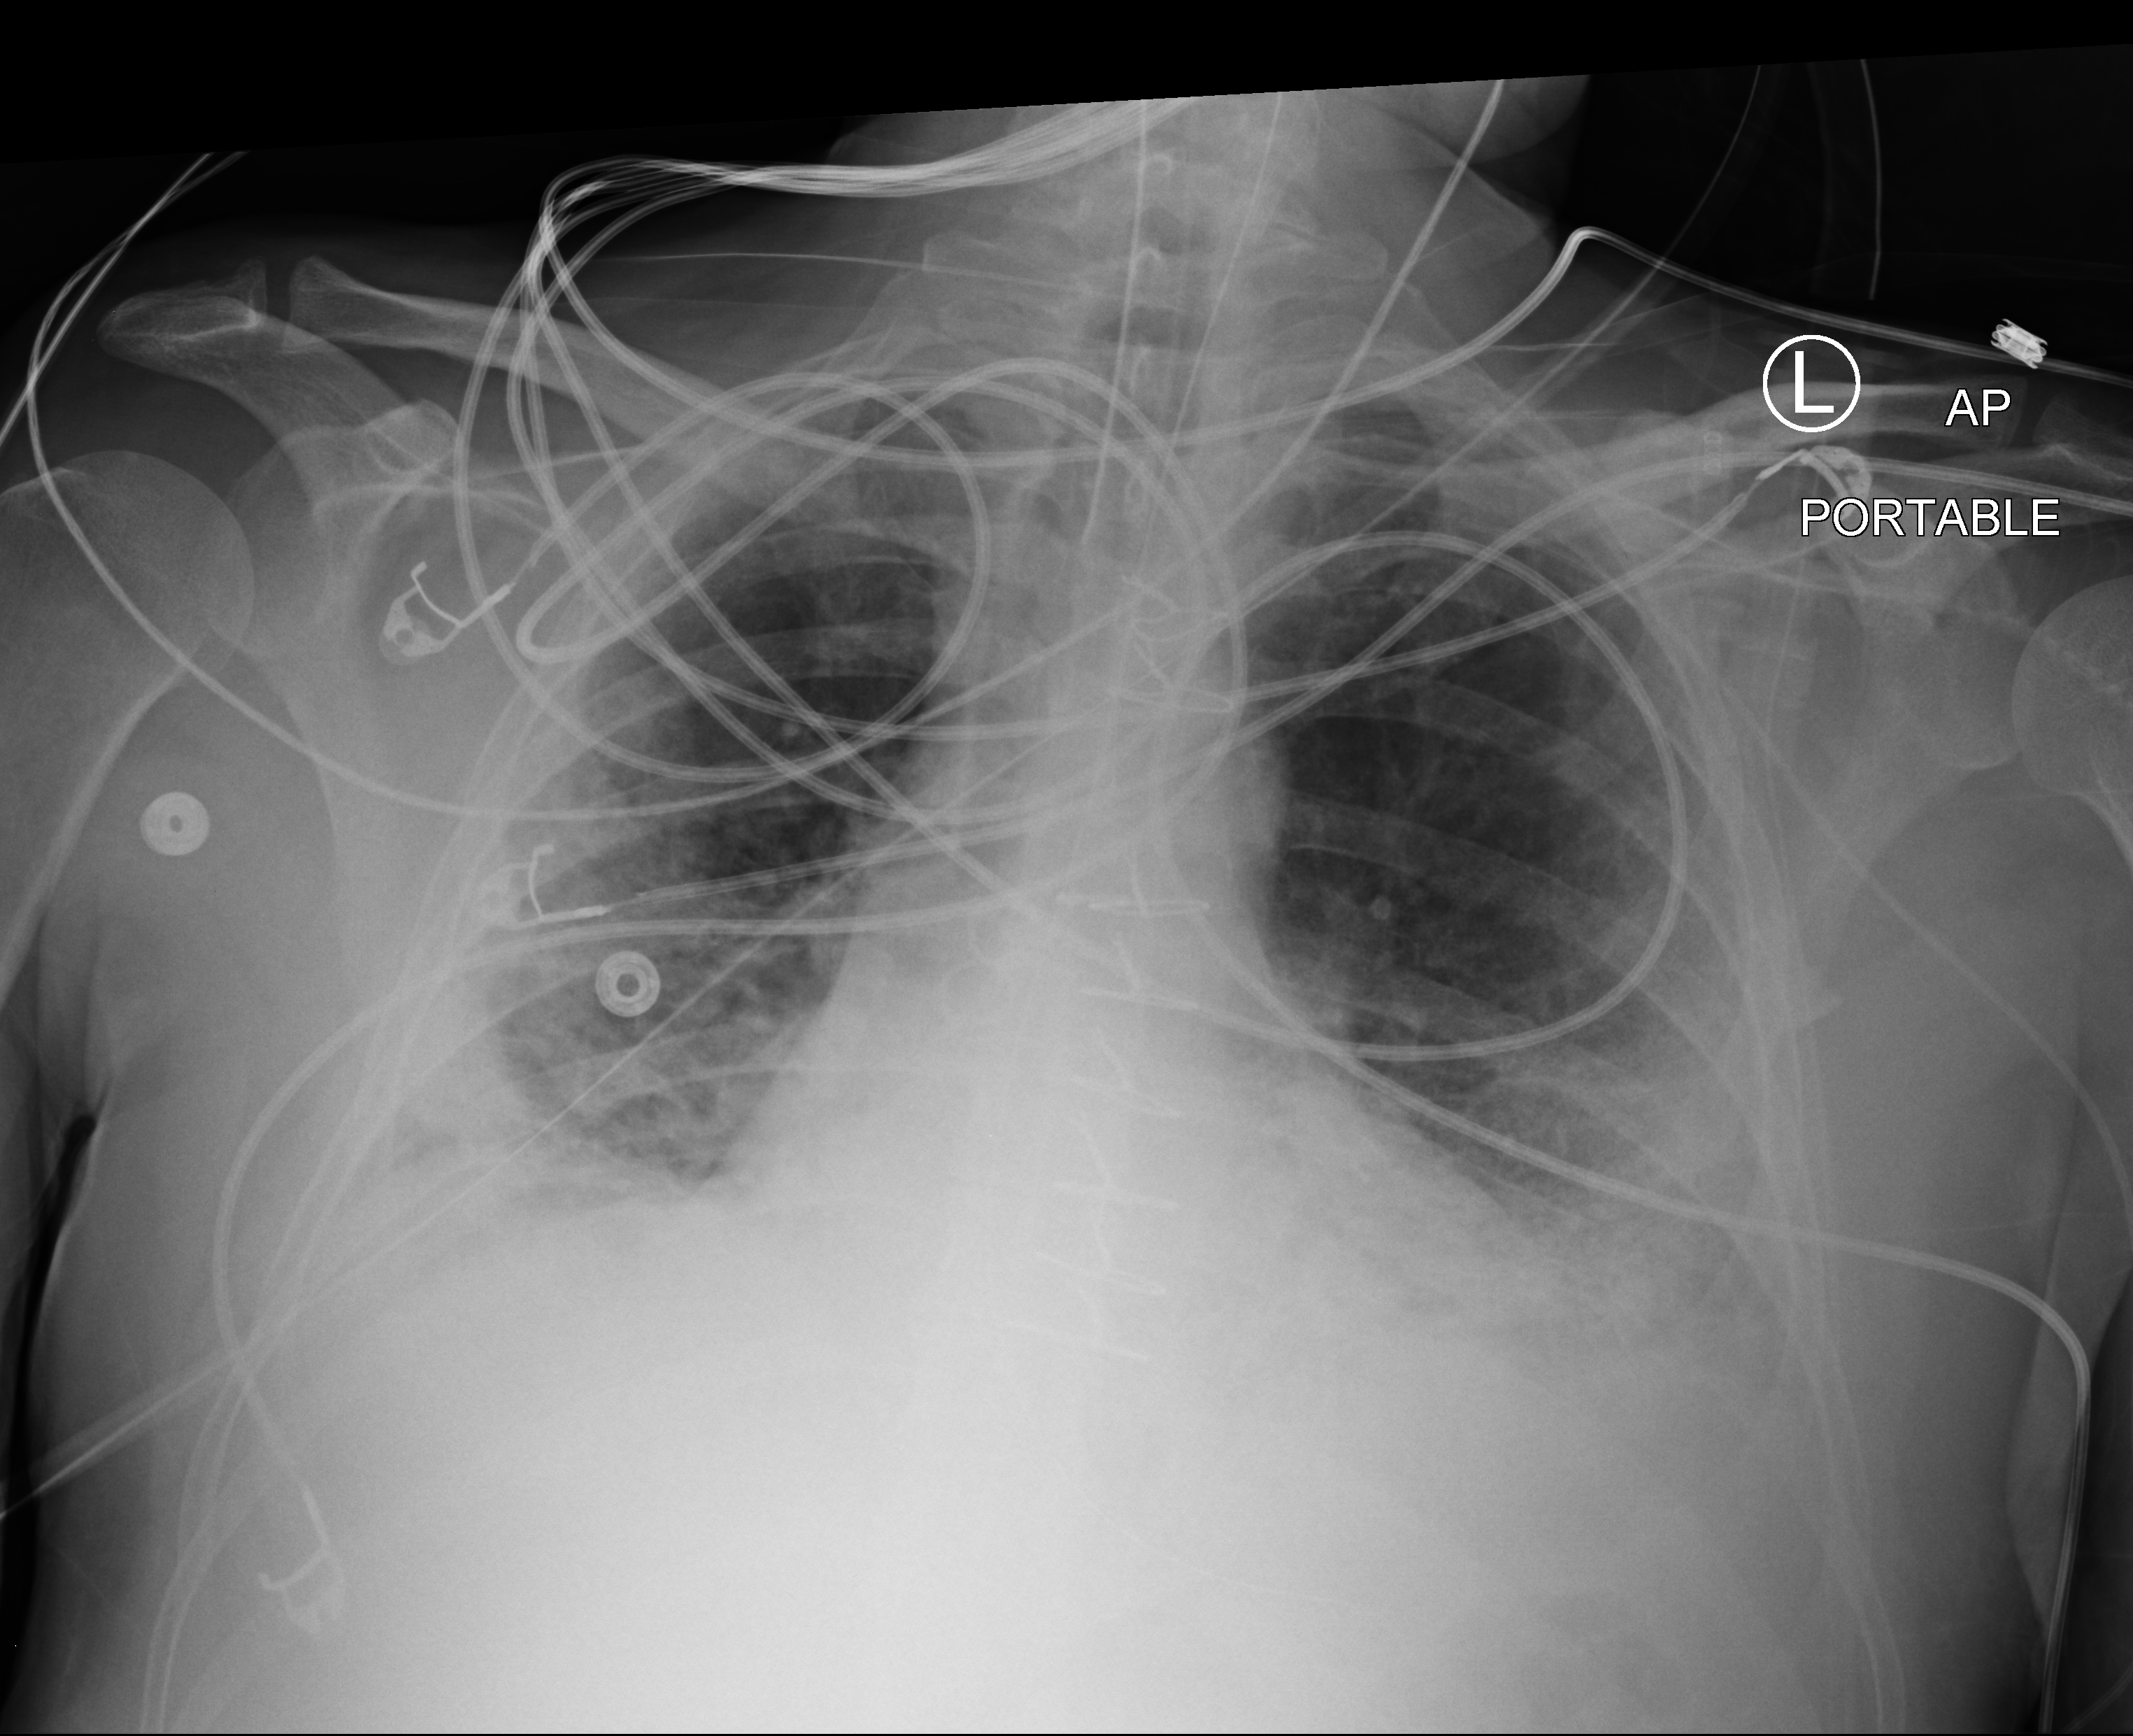
Chest X-ray (portable), anteroposterior (AP) projection. Patient hospitalised with COVID-19; male, aged 18–59 years.
From the hospital-stay record, not from the radiograph (when in the stay this image was taken is not recorded): length of hospital stay: 63 days.